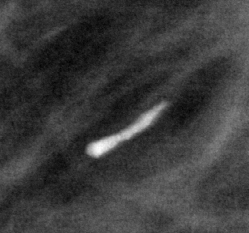
Region of interest cut from a scanned film mammogram (one marked finding); right breast; MLO view; BI-RADS breast density category 1 (scale 1–4).
- Finding: calcifications, morphology large rodlike, distribution segmental; BI-RADS assessment category 2; benign; no additional work-up was recommended (benign without callback).